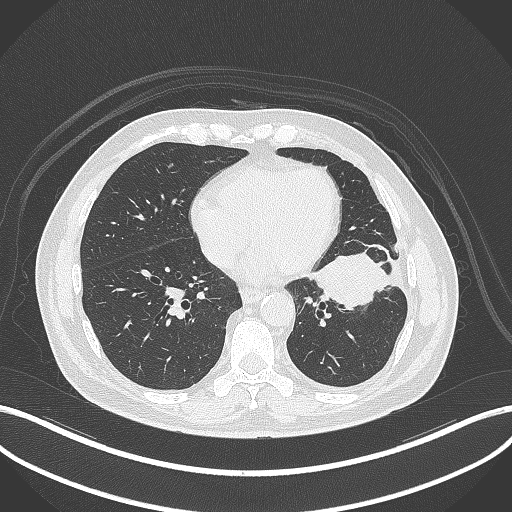
Chest CT, one axial slice; position 133 of 230 along the scan axis; lung window (W 1500 / L -600 HU); 1 mm slice thickness; 512 × 512 image matrix, field of view 400 × 400 mm. Patient: male, 68 years. Case-level facts recorded for this patient, not image findings: clinical TNM (as recorded): T2b N0 M0.
Outlined on this slice (rectangle marked by the reading radiologist):
- lung tumour (recorded histology: squamous cell carcinoma): box from (x=307, y=247) to (x=390, y=312) px